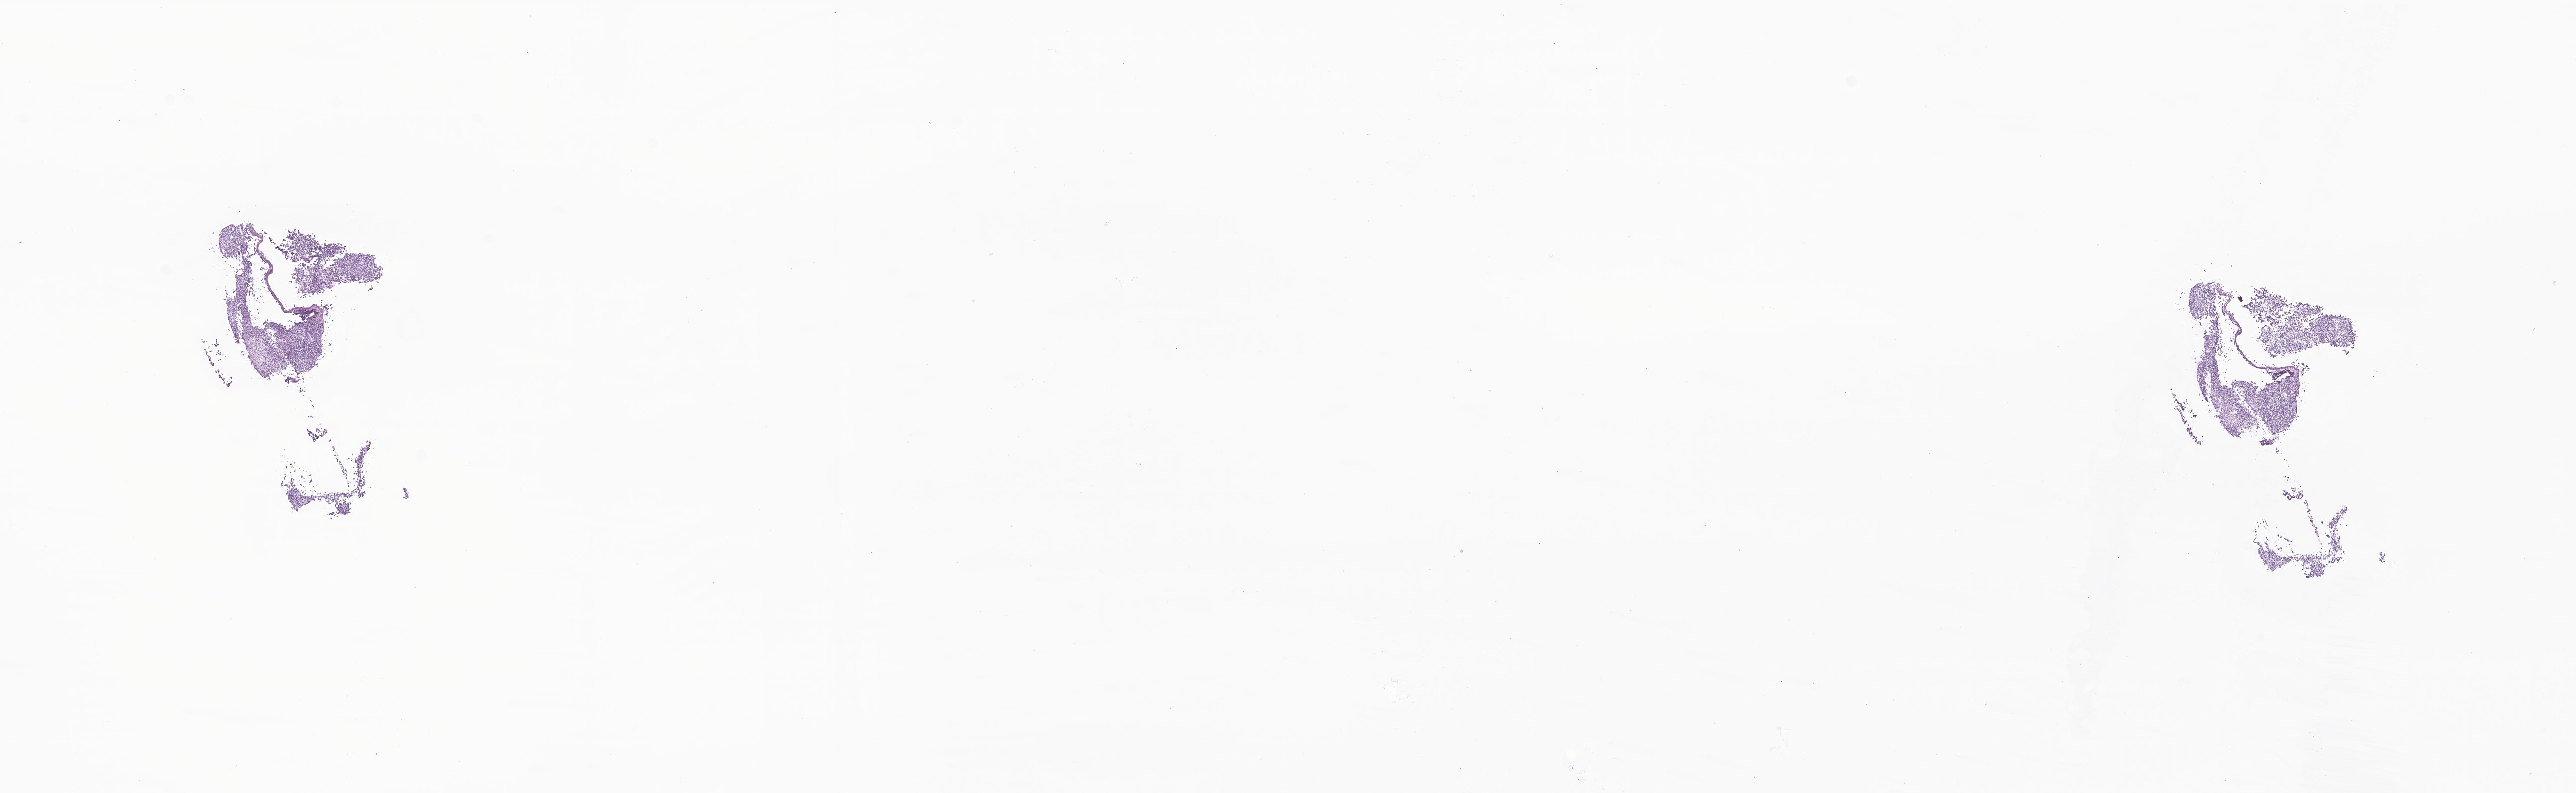
H&E whole-slide image of tumor tissue from the cerebellum — a low-resolution overview of the entire scanned area, about 21.8 x 6.7 mm; cryosection (OCT / tissue freezing medium). Male patient, age 50 months (4 years 2 months).
Diagnosis: Medulloblastoma, NOS.